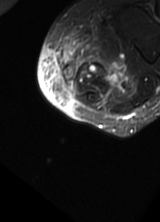
MRI of an extremity soft-tissue mass, one axial slice; slice 3 of 69 in the series (ordered by position); T2-weighted fat-saturated; MR volume resampled by the dataset authors to the PET/CT grid (not the native acquisition matrix); 160 × 222 image matrix, field of view 156 × 217 mm. Female patient. Case-level facts recorded for this patient, not image findings: histological type: pleomorphic leiomyosarcoma; grade: high; site of the primary tumour: left thigh.
Annotated regions visible in this slice (expert contour drawn on MRI and transferred to this co-registered scan by the dataset authors):
- gross tumour volume including surrounding oedema: bounding box [x1, y1, x2, y2] px = [59, 29, 133, 105]